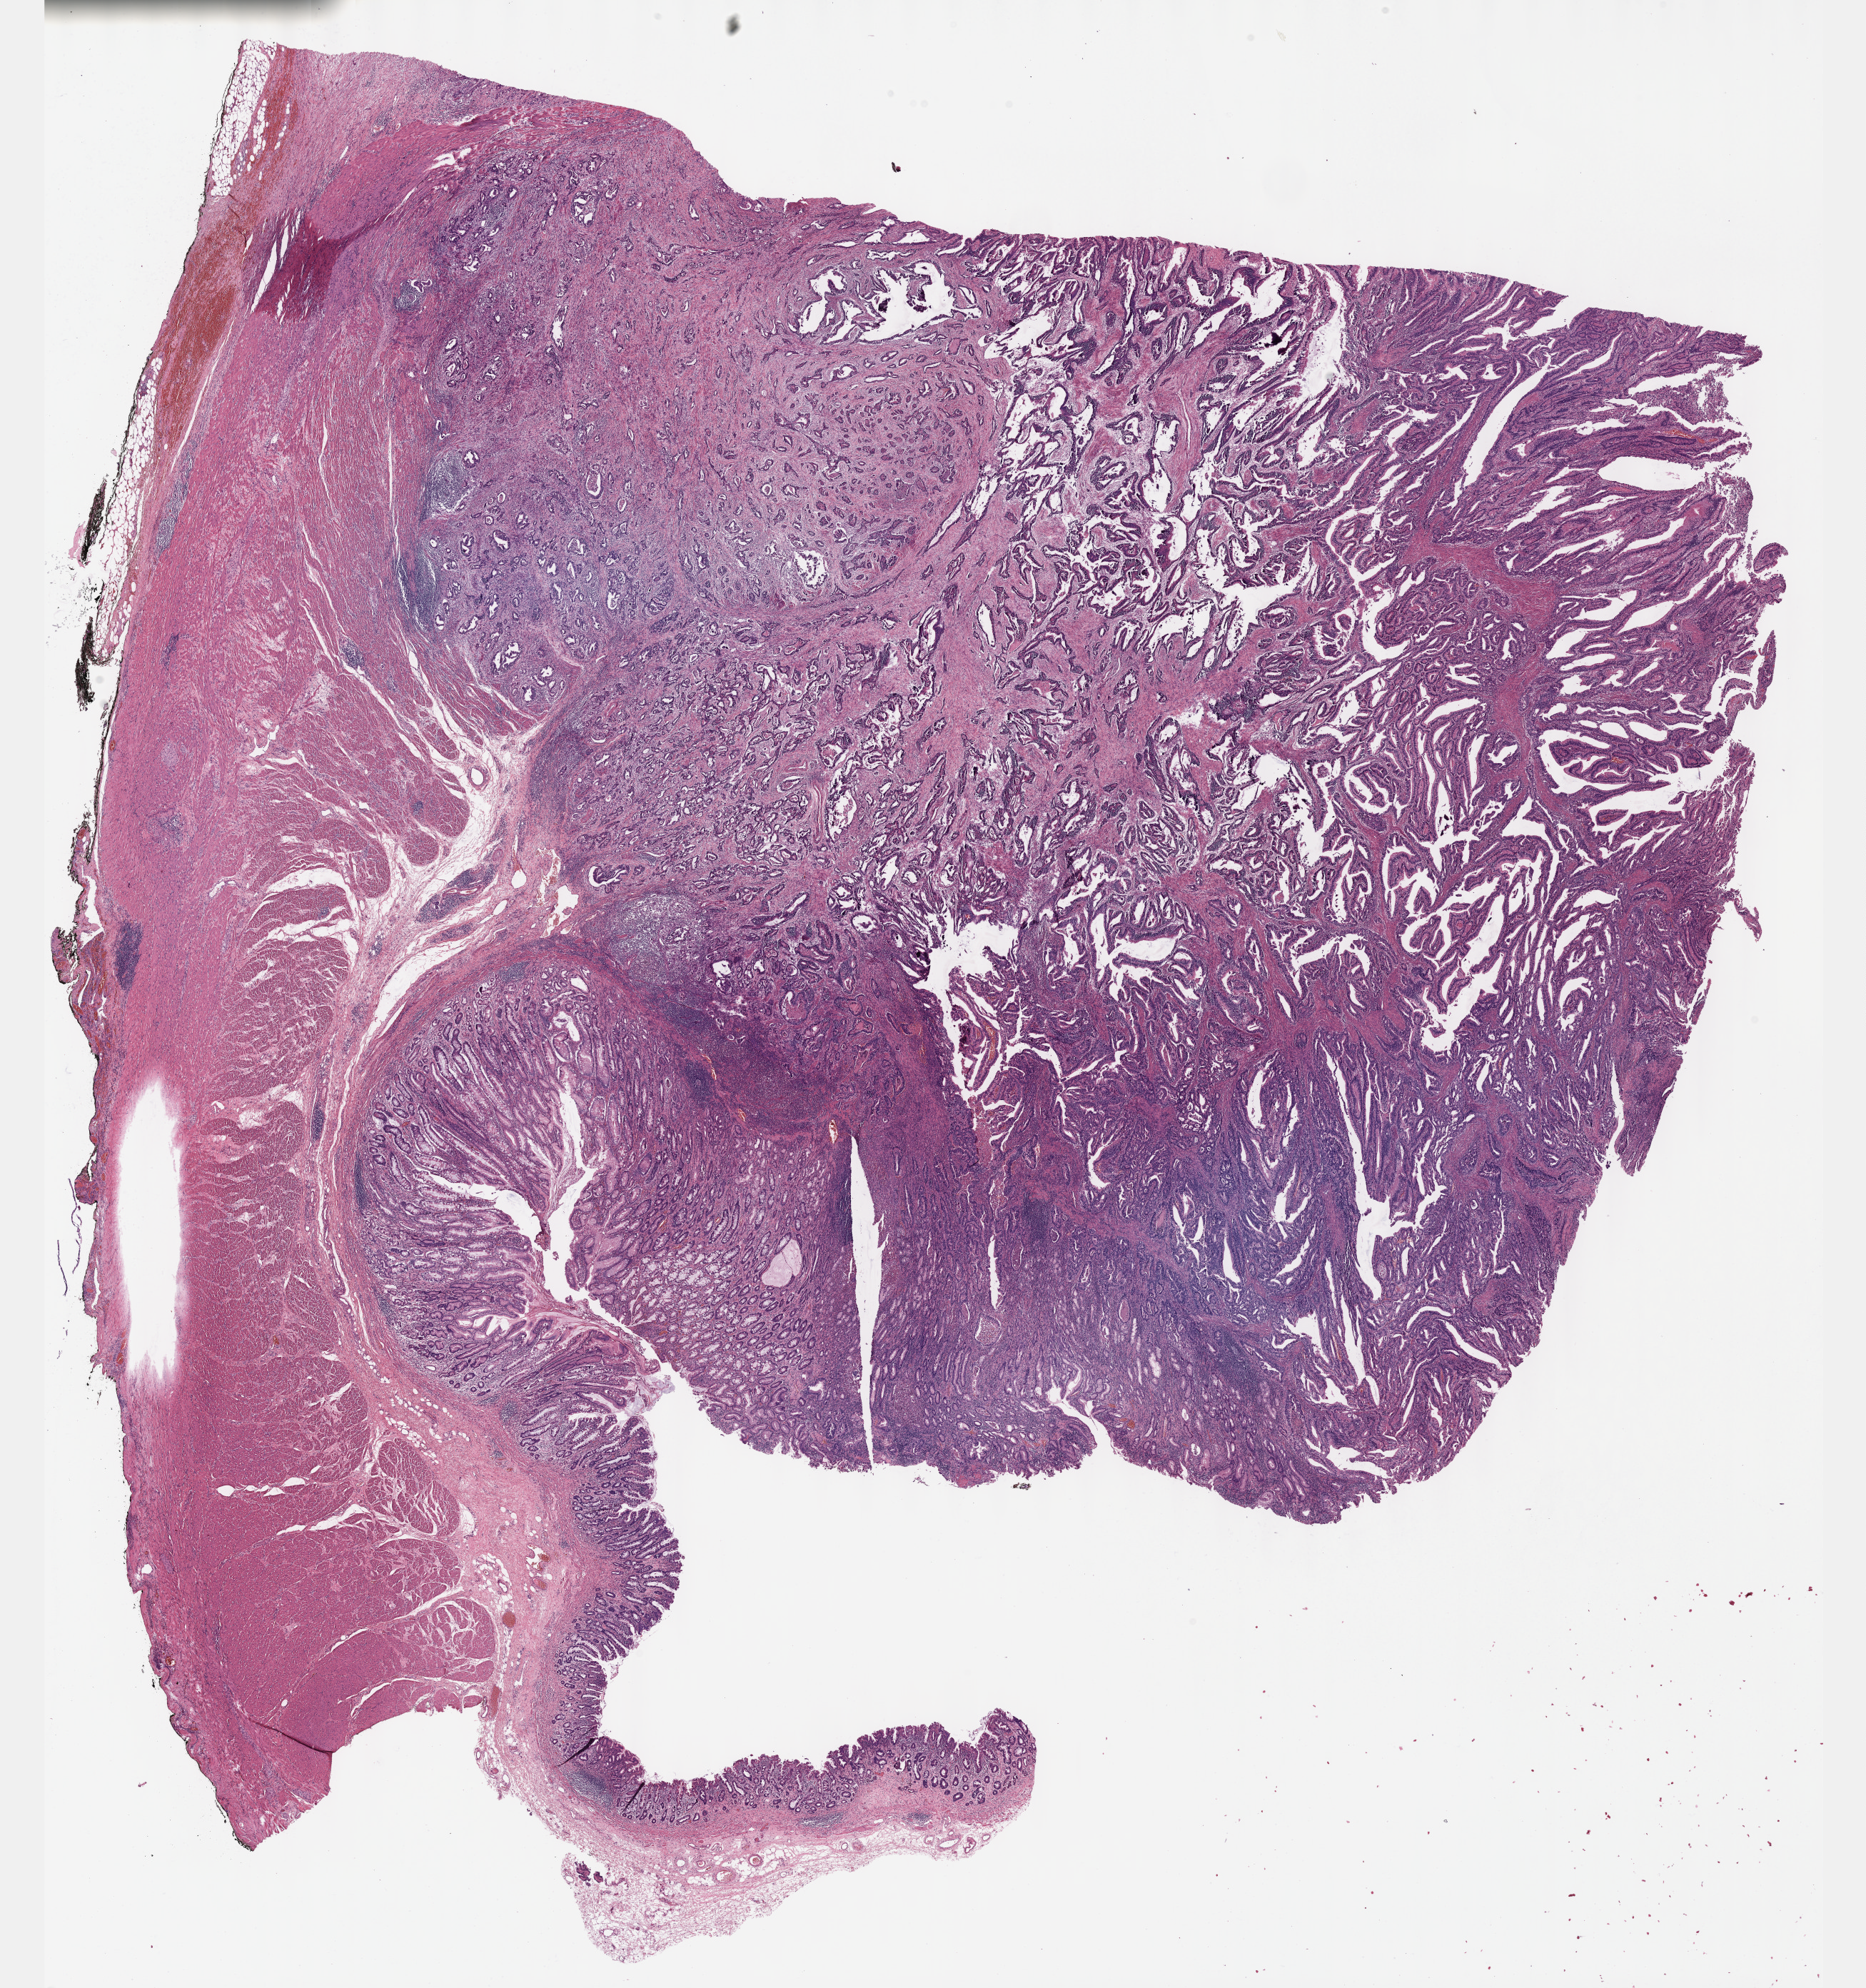
Whole-slide histology image, H&E, low-resolution overview of the scanned area, about 21.1 x 22.5 mm; FFPE section; primary tumour sample from the stomach. Patient: female, age at initial diagnosis 59 years. Histologic grade: G2 (moderately differentiated).
AJCC pathologic stage: IV (6th edition). Lymph nodes positive (case pathology): 18 of 32 examined. Diagnosis: Tubular adenocarcinoma (gastric antrum).